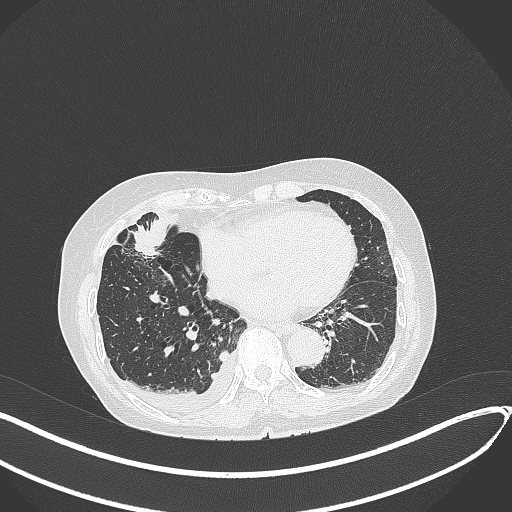
Chest CT, one axial slice. Slice 137 of 418 in the series (ordered by position). Reconstruction kernel B70f. 120 kVp. Lung window (W 1500 / L -600 HU). 1 mm slice thickness. 512 × 512 image matrix, field of view 400 × 400 mm. Female patient, age 75 years. From the clinical record (not read from this slice): clinical TNM (as recorded): T2a N3 M0.
Structures marked on this image (bounding box drawn by a radiologist):
- lung tumour (recorded histology: adenocarcinoma): bounding box [x1, y1, x2, y2] px = [126, 222, 163, 262]